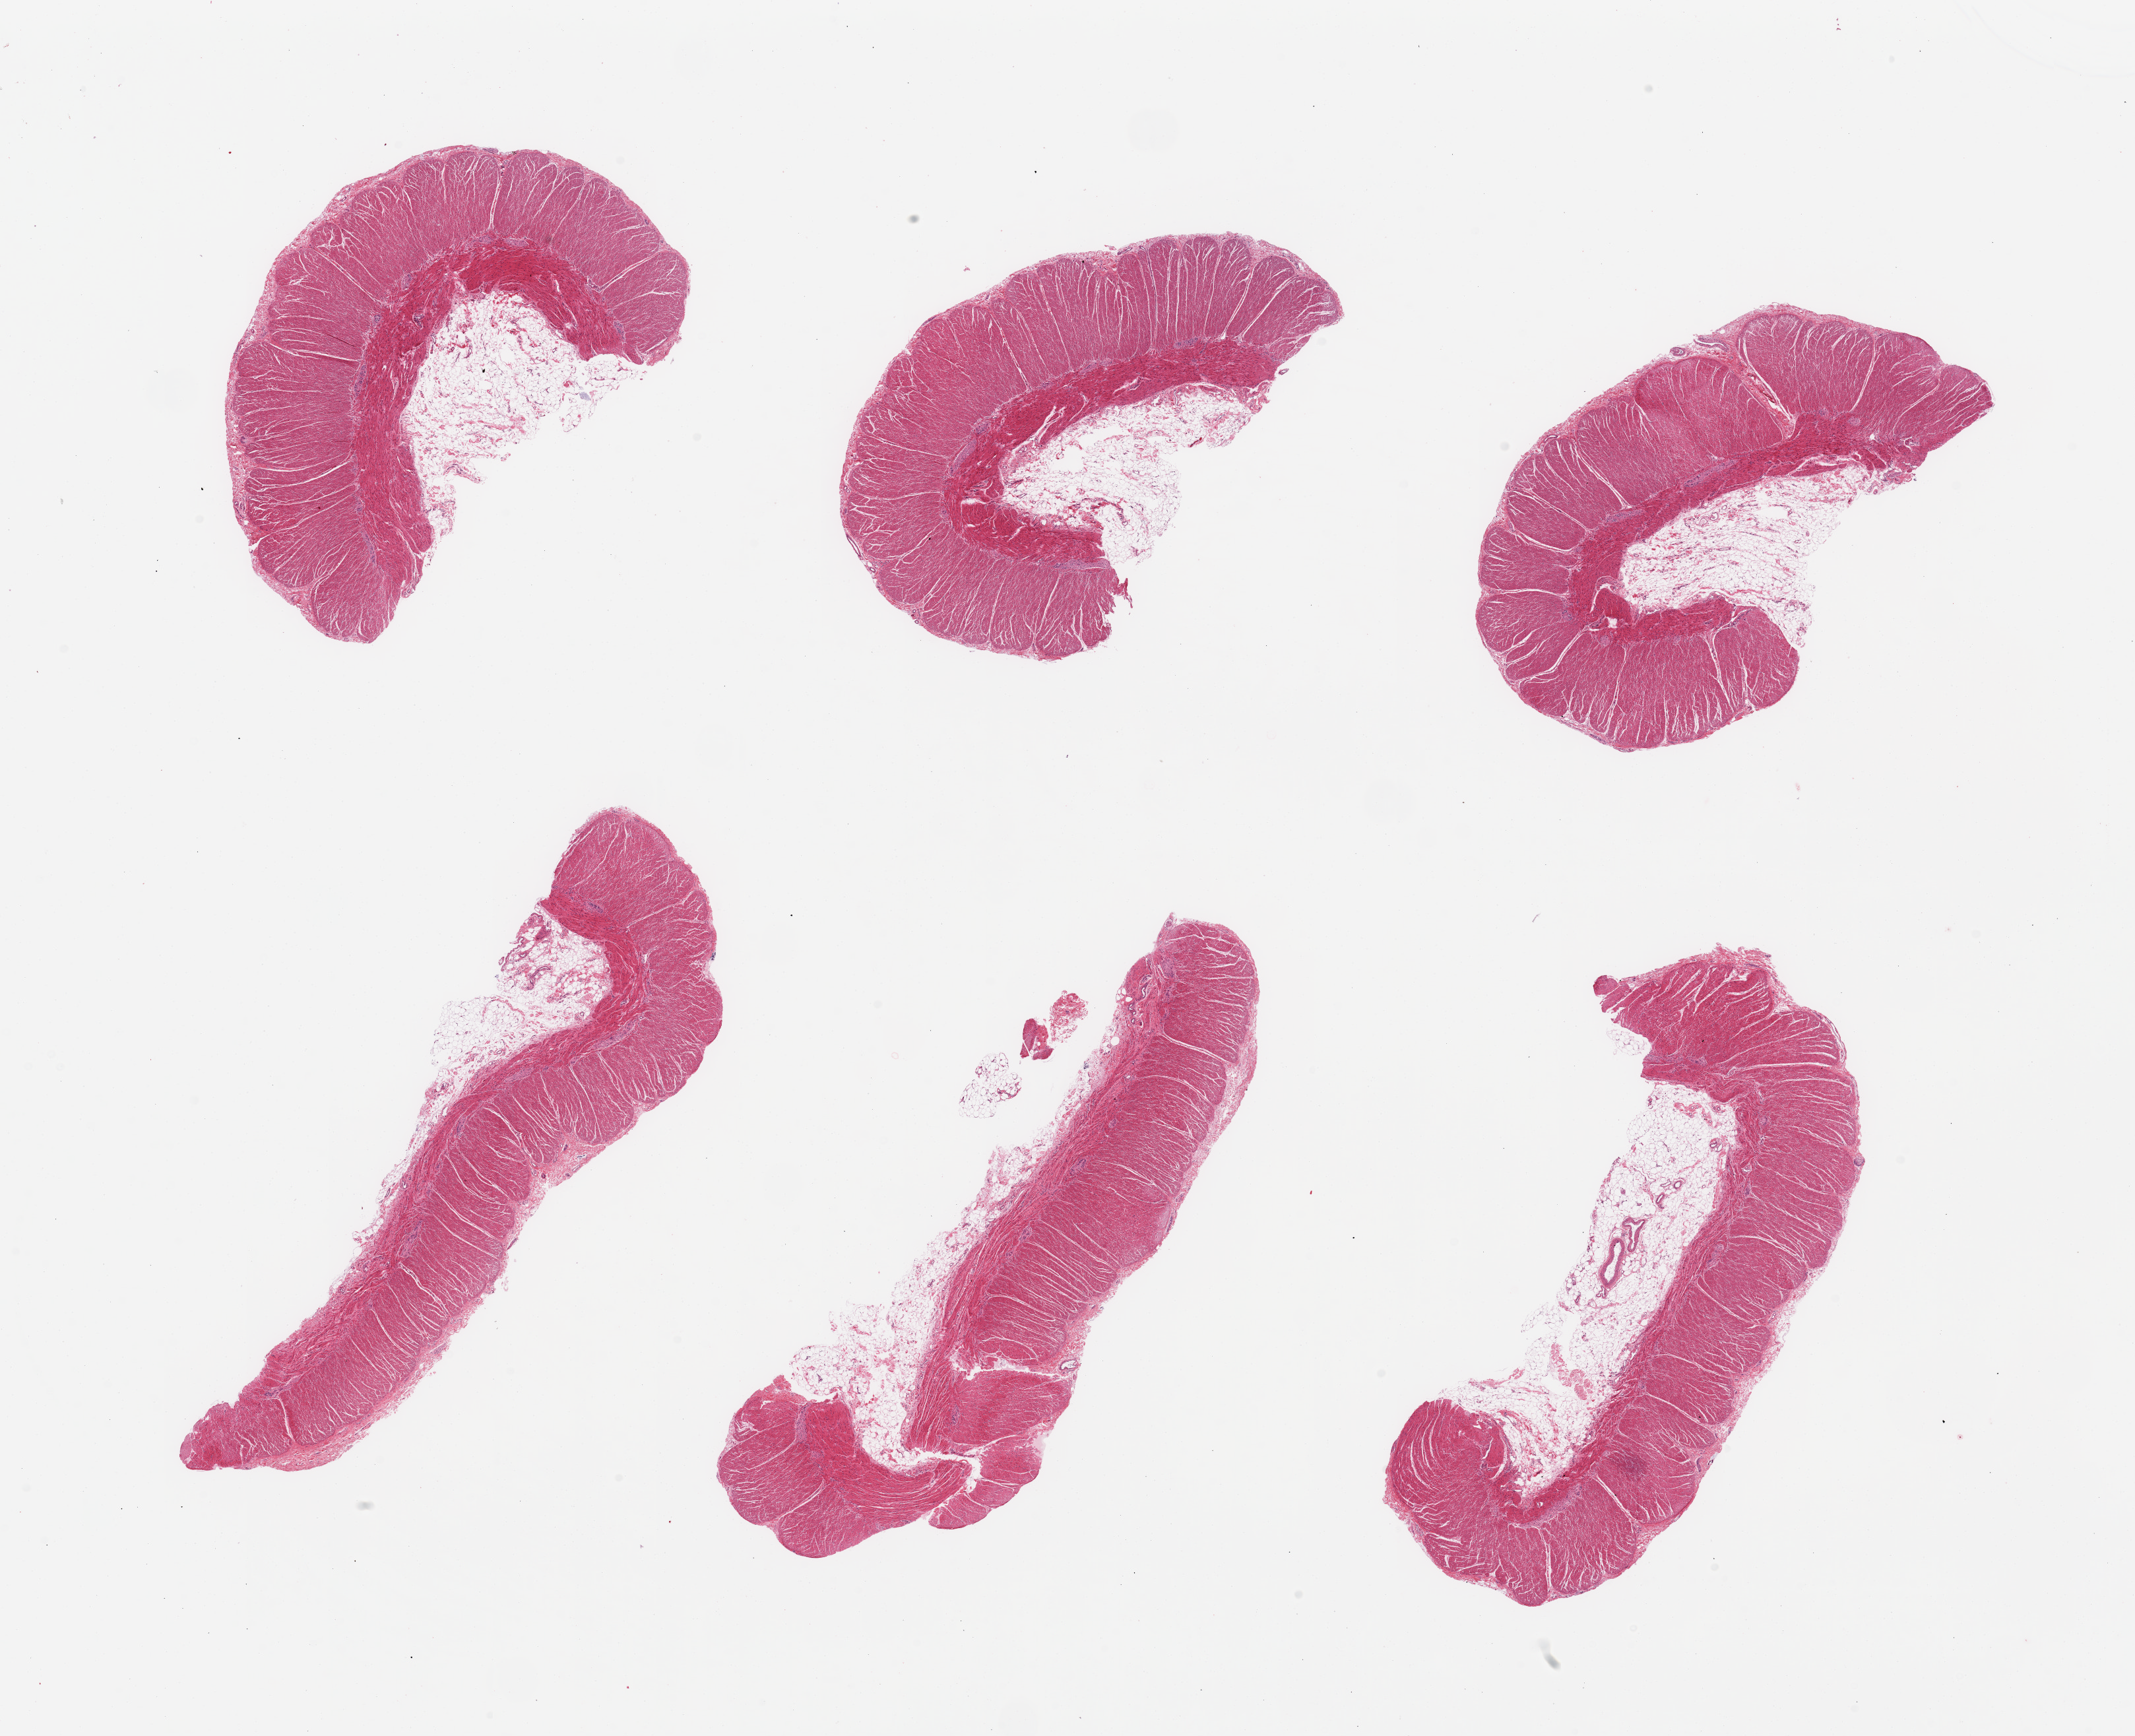
Whole-slide image, H&E stain, brightfield — shown as a low-resolution overview of the whole scanned area (about 25.6 x 20.8 mm, from a 20x scan); PAXgene-fixed, paraffin-embedded tissue; sampled site (target tissue): sigmoid colon; donor tissue sample. Donor: male.
- review note (as recorded): 6 pieces, confirmed target muscularis